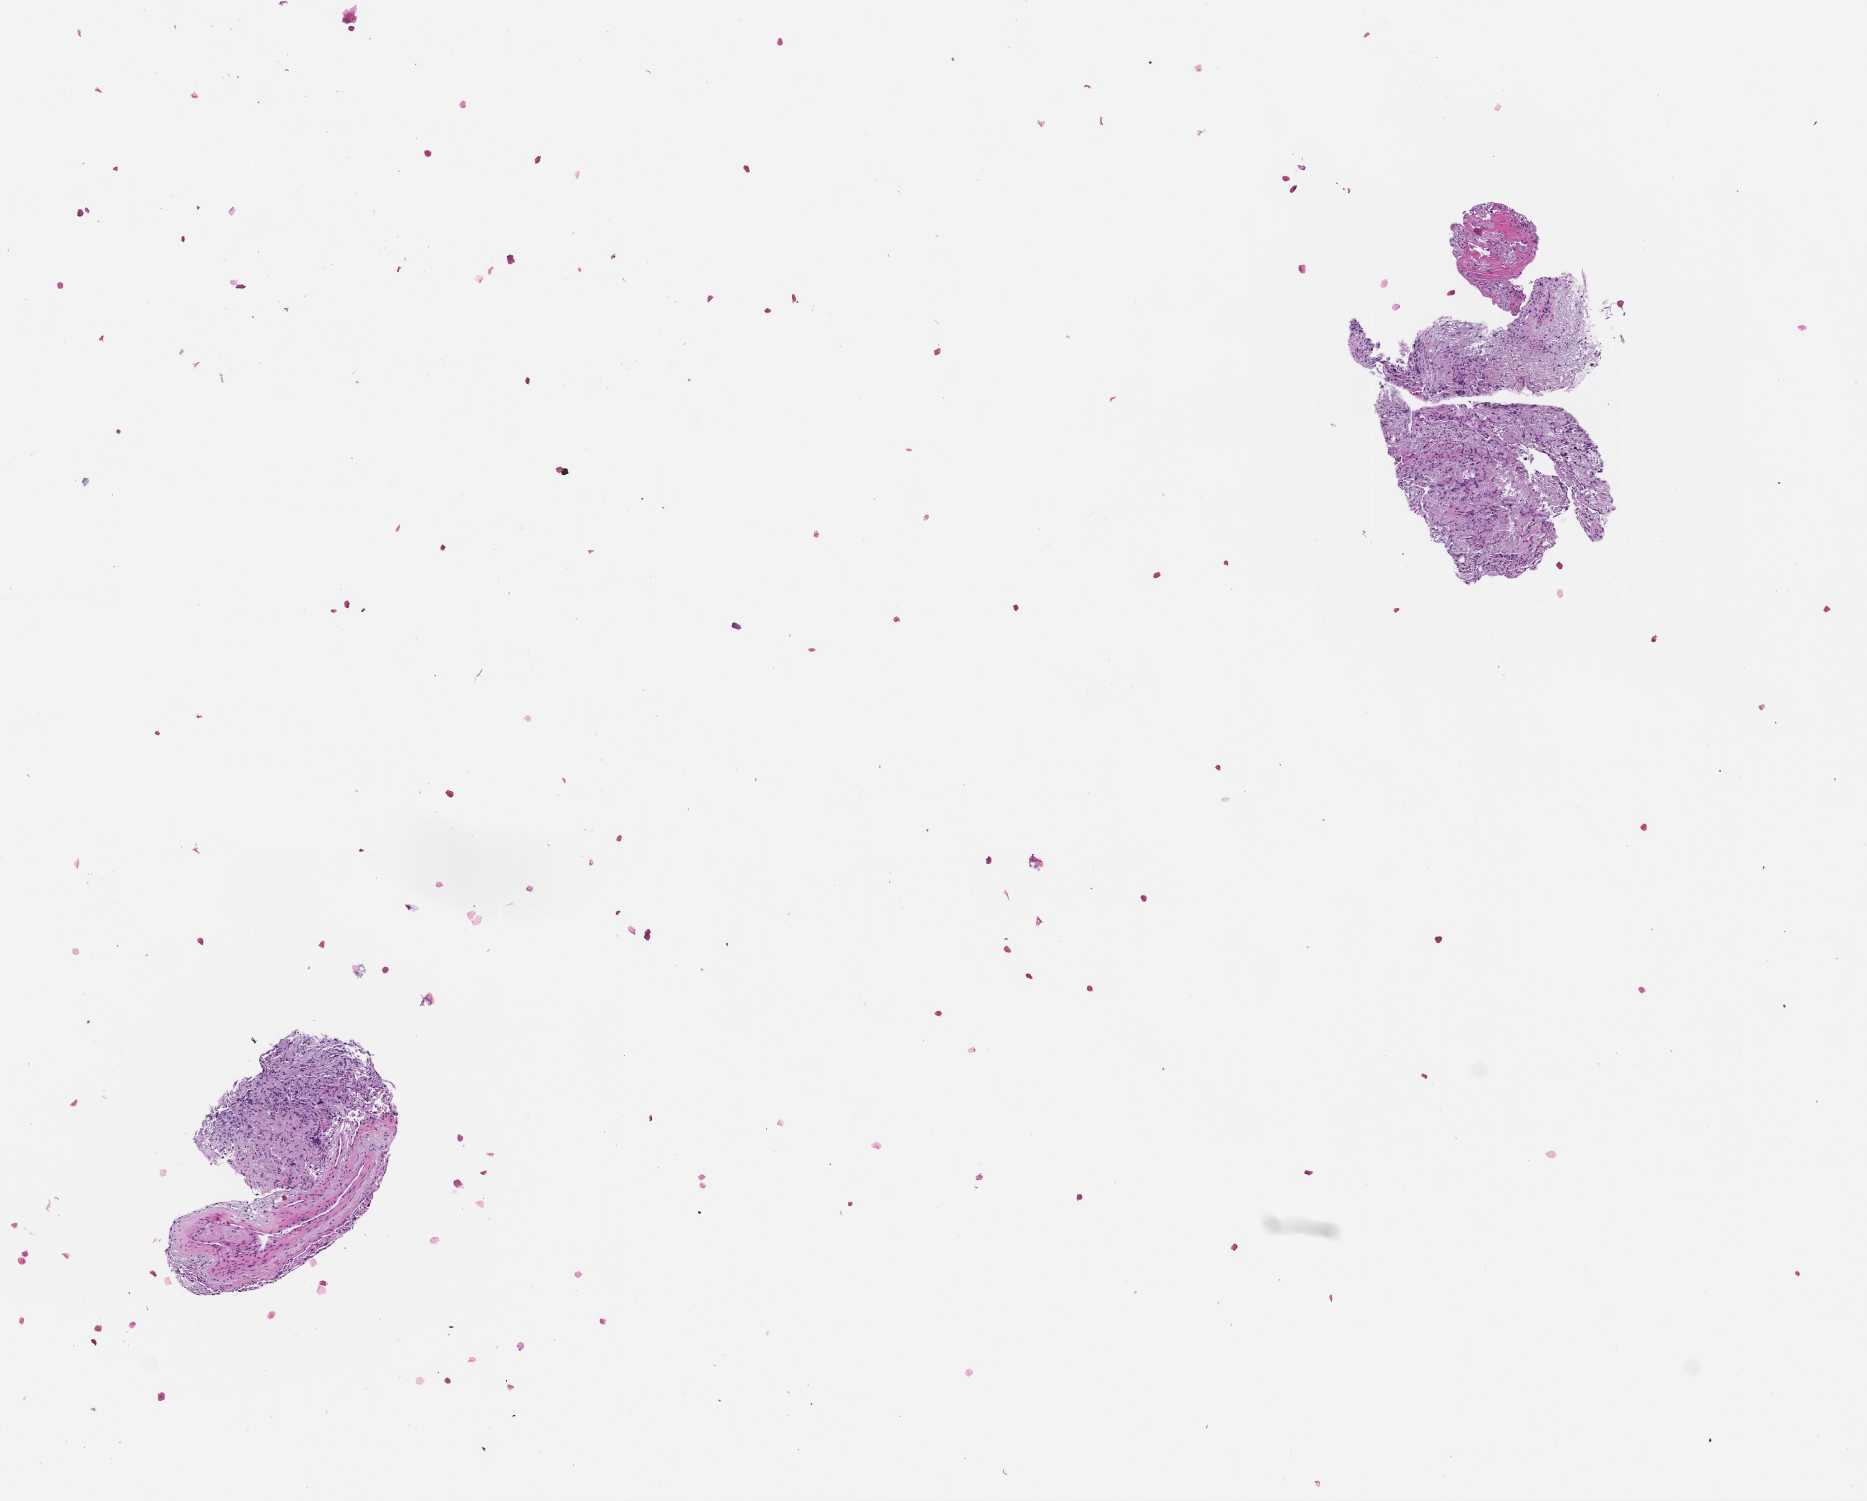
Whole-slide image, H&E stain, a low-resolution overview of the entire scanned area, about 7.5 x 6.1 mm. Formalin-fixed, paraffin-embedded (FFPE) tissue. Site: lung. Patient sex: male.
This section: primary tumour tissue. Diagnosis: Non-Small Cell Lung Carcinoma.